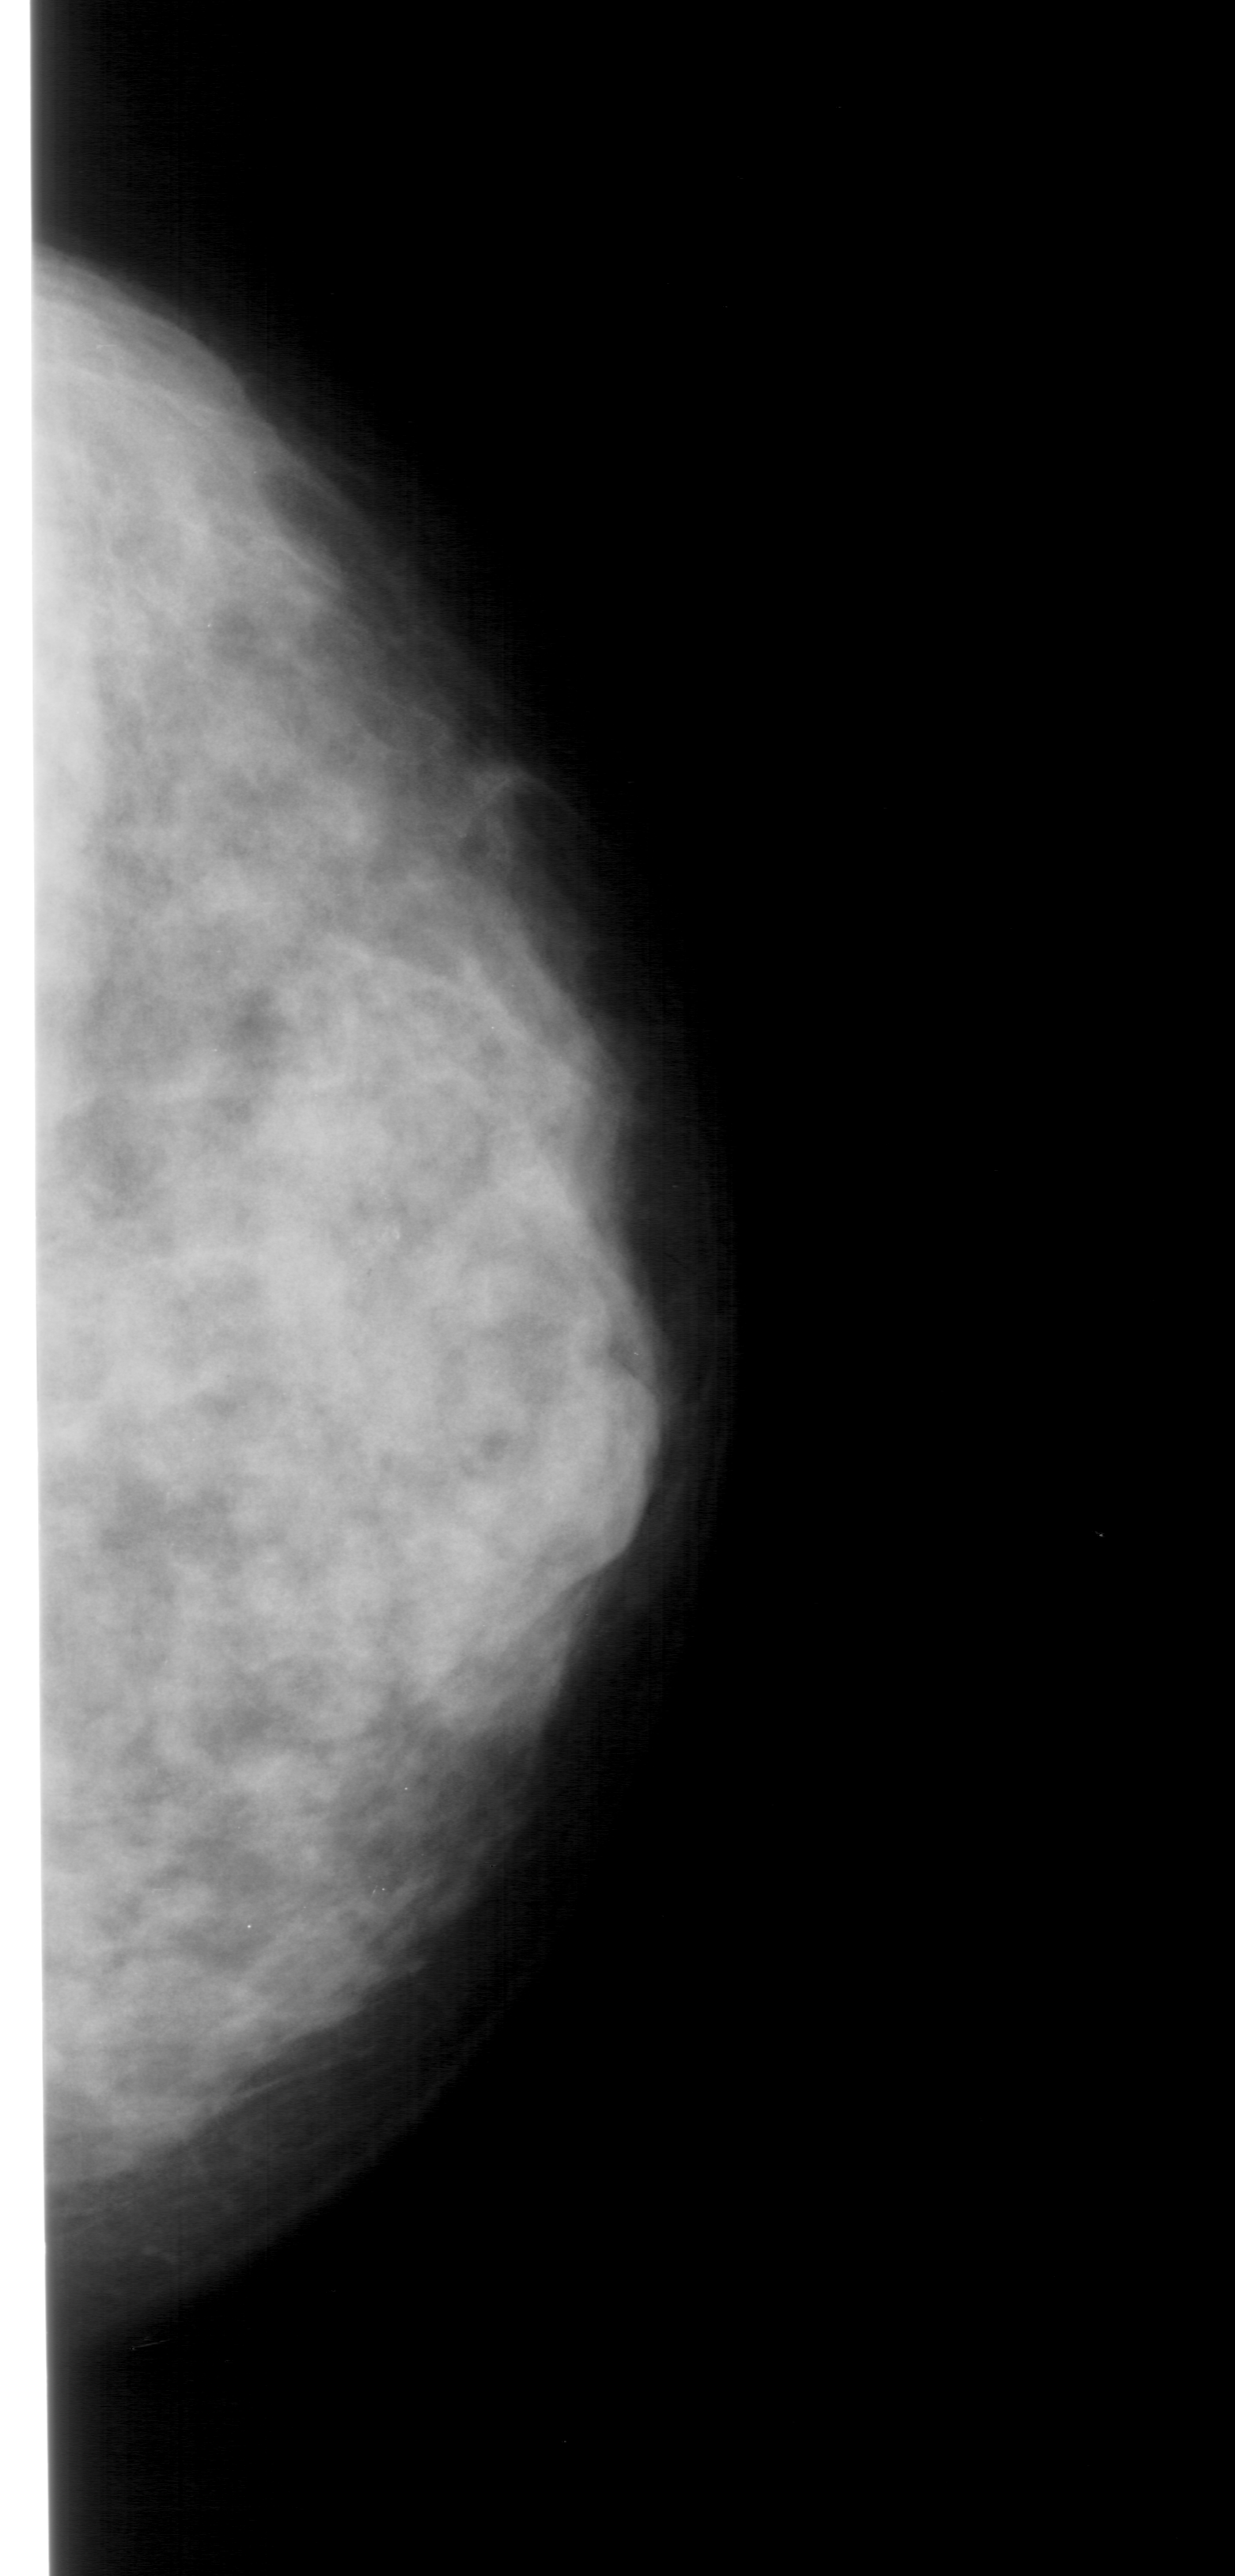
Digitized screen-film mammogram; right breast; craniocaudal (CC) view; BI-RADS breast density category 3 (scale 1–4).
Finding: calcifications, morphology pleomorphic, distribution clustered; BI-RADS assessment category 4; pathology (as recorded): benign.